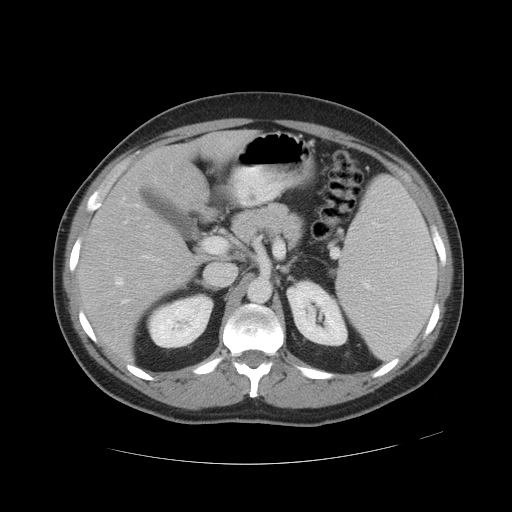
Contrast-enhanced abdominal CT, one axial slice; slice 29 of 49 in the series (ordered by position); reconstruction kernel STANDARD; 120 kVp; intravenous contrast given; soft-tissue window (W 400 / L 40 HU); 512 × 512 image matrix. Male patient, age 42 years. Case-level facts recorded for this patient, not image findings: diagnosis: colorectal cancer liver metastases, imaged before liver resection; multiple liver metastases: yes; largest metastasis: 2.8 cm; disease in both lobes: yes.
Outlined on this slice (outlined manually by an expert reader):
- hepatic veins: box from (x=116, y=198) to (x=149, y=285) px
- liver: (x=81, y=133)–(x=243, y=356)
- planned liver remnant (the part of the liver to remain after resection): (x=81, y=133)–(x=242, y=356)
- portal vein (with intrahepatic branches): (x=143, y=255)–(x=158, y=261)